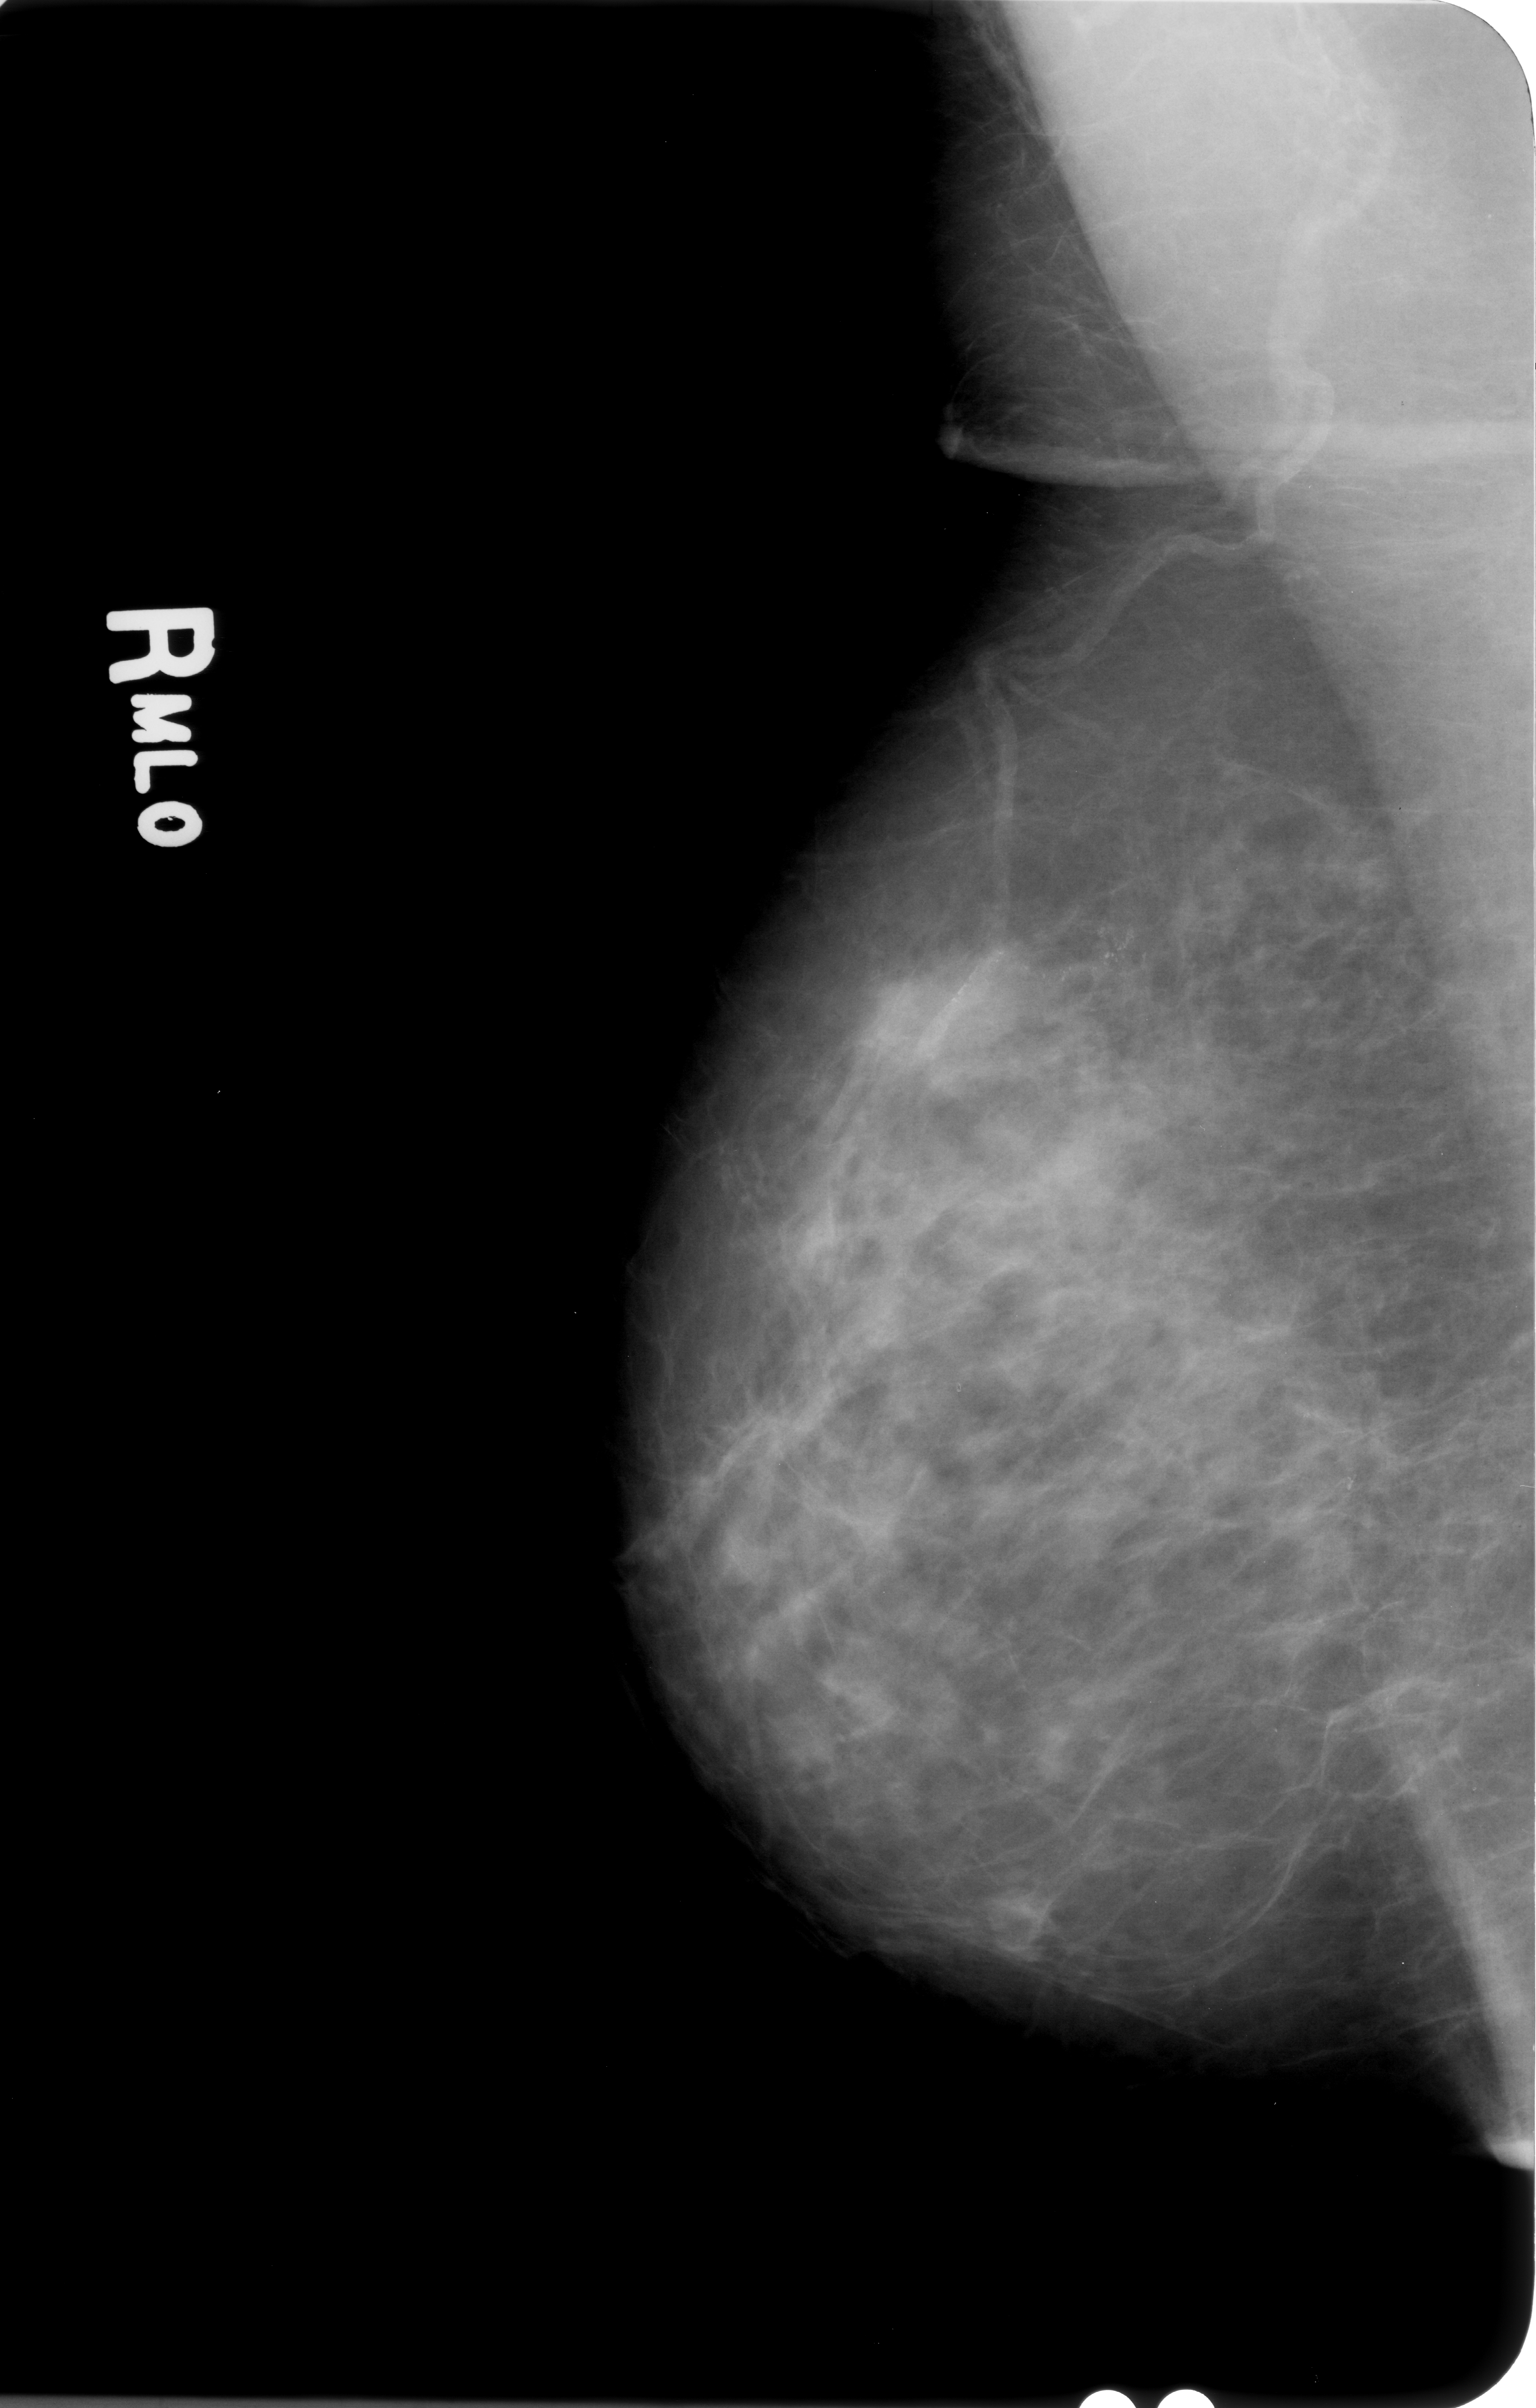
Digitized screen-film mammogram, right breast, mediolateral oblique (MLO) view.
Marked findings (only marked abnormalities are described; nothing is implied about the rest of the image): calcifications, morphology pleomorphic, distribution clustered / linear; BI-RADS assessment category 4; subtlety rating 3 on a 1 (subtle) to 5 (obvious) scale; pathology result (as recorded, not read from the image): benign.